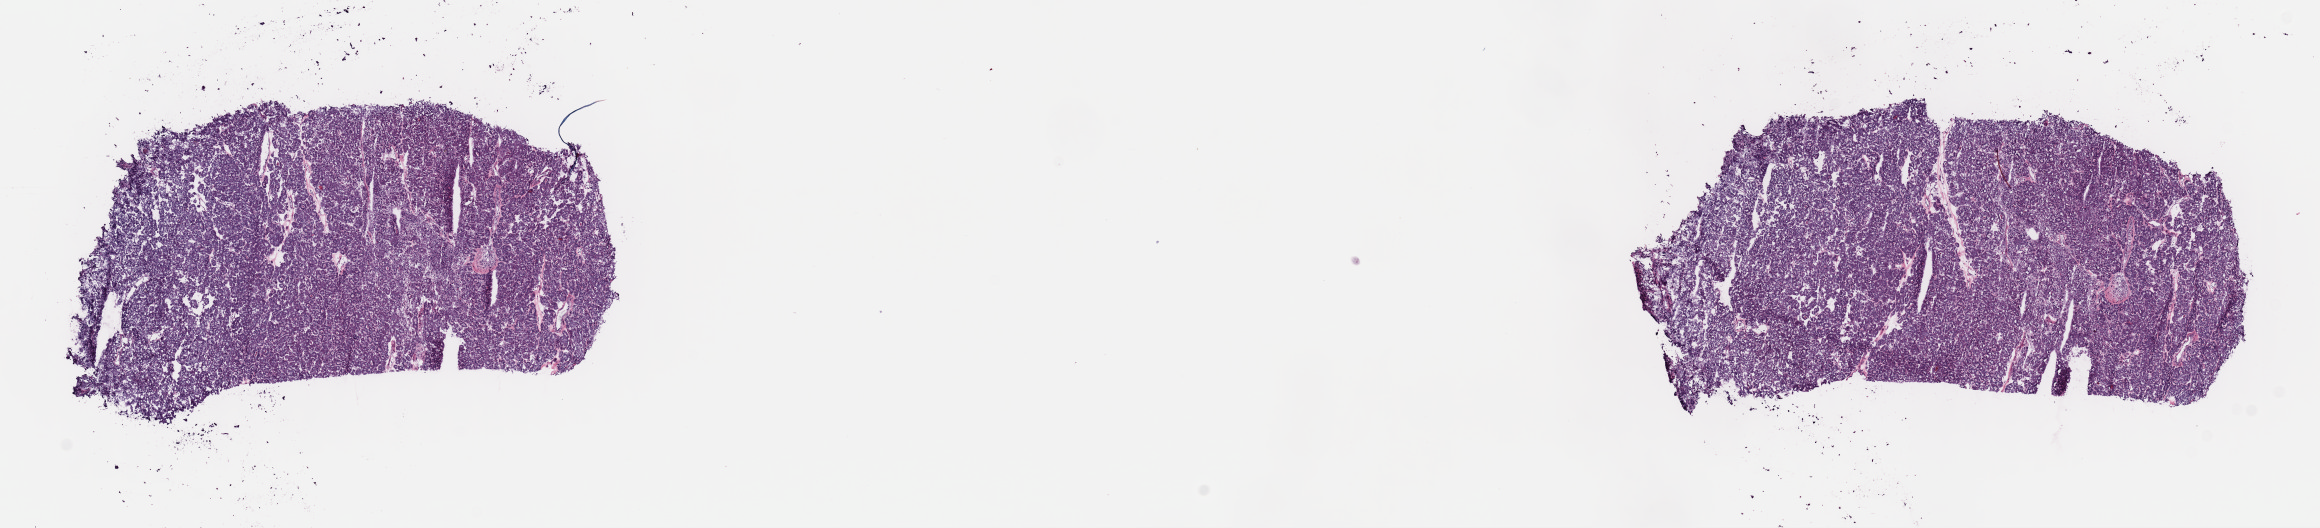
H&E-stained whole-slide image, whole scanned area (about 18.3 x 4.2 mm, acquisition: 40x scan) shown as a low-resolution overview, frozen section from the top of the tissue portion, sample: primary tumour, thyroid. Patient: female, age at initial diagnosis 57 years. Slide review estimates, as recorded: tumour cells 90%, tumour nuclei 90%, normal cells 0%, stromal cells 10%, necrosis 0%. Inflammatory infiltration, as recorded: lymphocyte infiltration 2%, monocyte infiltration 0%, neutrophil infiltration 0%.
Laterality: right. AJCC pathologic stage: II (7th edition). Histologic diagnosis: Papillary adenocarcinoma, NOS (thyroid gland).